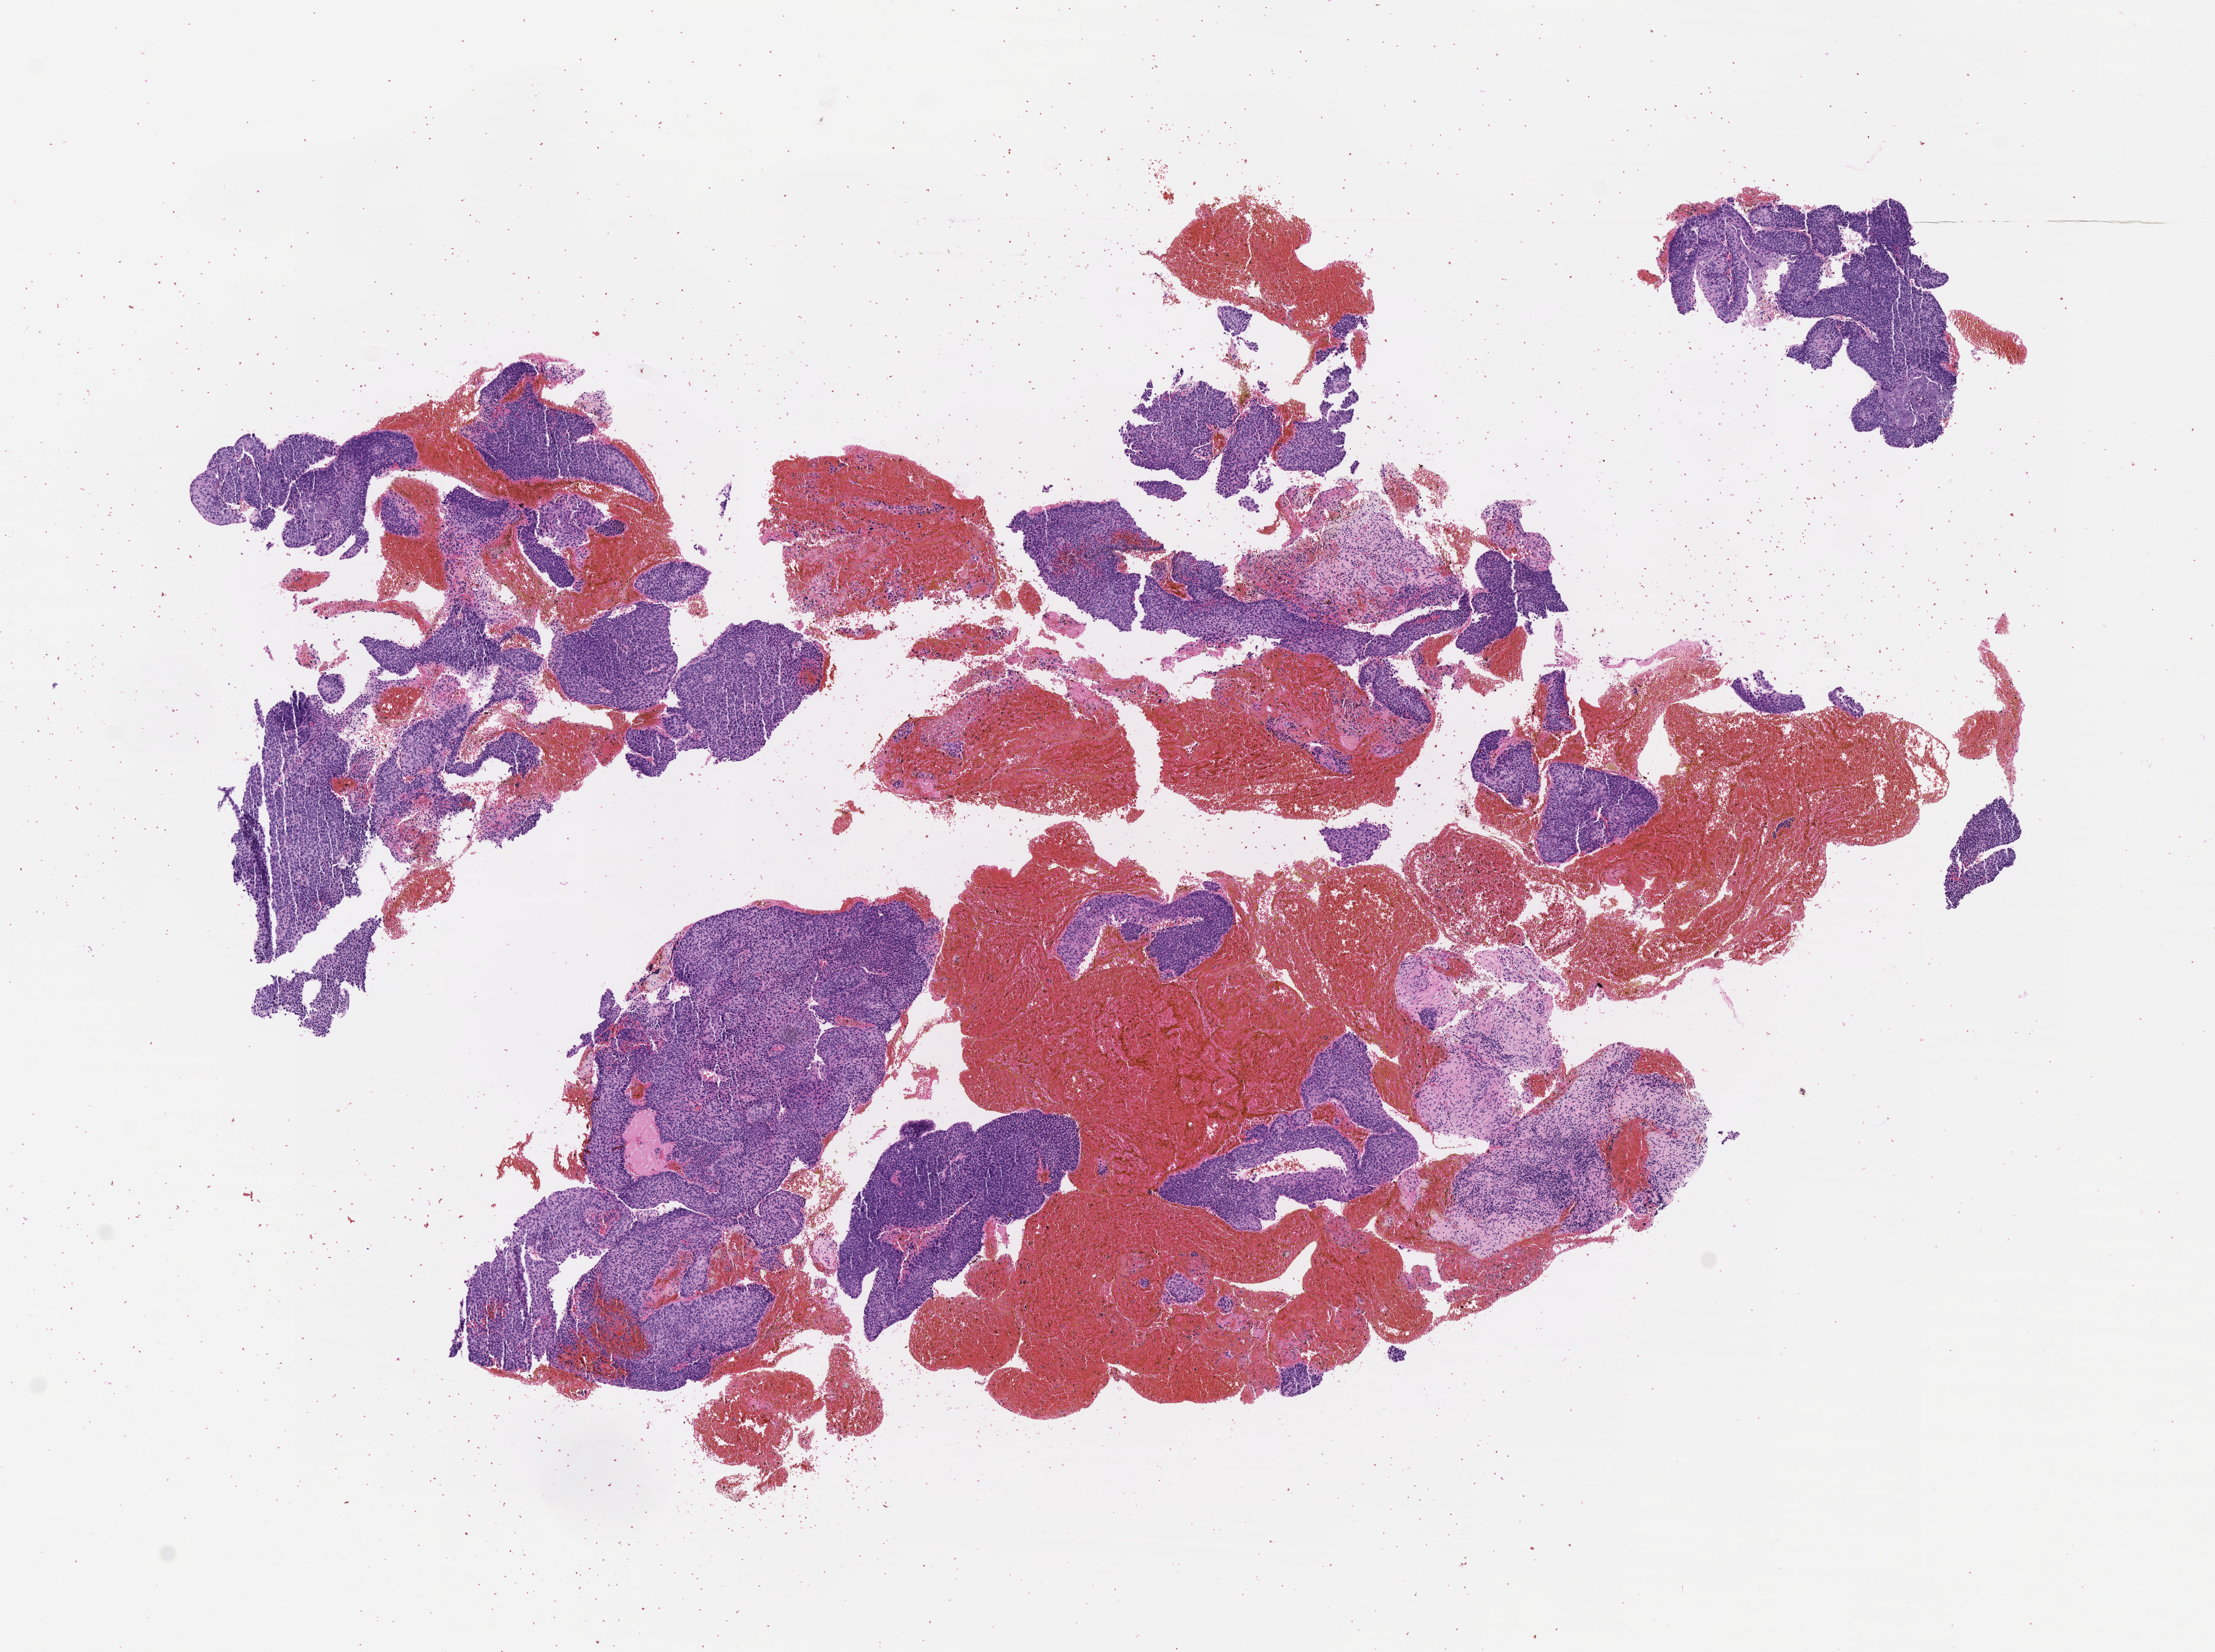
Haematoxylin and eosin whole-slide image, a low-resolution overview of the entire scanned area, about 7.5 x 5.6 mm. Specimen: tumor tissue. Anatomic site: cervix. Female patient, 50 years old.
* diagnosis: Squamous cell carcinoma, large cell, nonkeratinizing, NOS